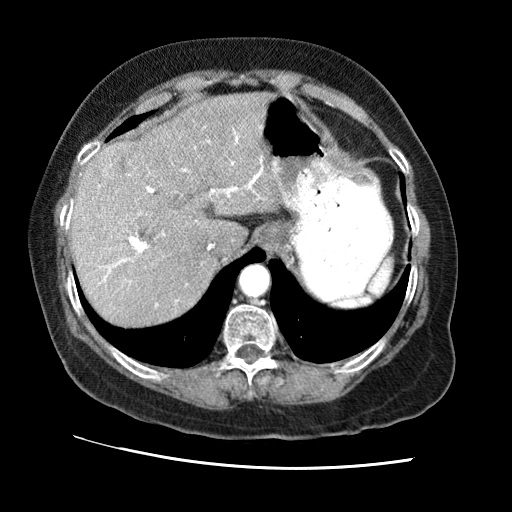
Contrast-enhanced abdominal CT (liver protocol), one axial slice. Position 50 of 65 along the scan axis. Soft-tissue window (W 400 / L 40 HU). 2.5 mm slice thickness. 512 × 512 image matrix, field of view 340 × 340 mm. Case-level facts recorded for this patient, not image findings: diagnosis: hepatocellular carcinoma (patient treated with transarterial chemoembolisation; whether this scan precedes or follows treatment is not stated here); TNM stage (as recorded): Stage-II; Child-Pugh class: A; tumour differentiation: no biopsy.
Structures marked on this image (semi-automatically segmented with operator editing):
- liver parenchyma outside the tumour (the mass and vessels are separate outlines, so this box may not span the whole liver): bounding box [x1, y1, x2, y2] px = [68, 92, 280, 326]
- mass: [97, 143, 136, 179]
- liver vessels: [69, 131, 263, 306]